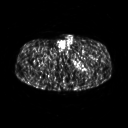
FDG PET of an extremity soft-tissue mass (from a PET/CT study), one axial slice. Position 263 of 267 along the scan axis. 3.27 mm slice thickness. 128 × 128 image matrix, field of view 500 × 500 mm. Patient: male, 27 years. From the clinical record (not read from this slice): histological type: extraskeletal osteosarcoma; grade: high; site of the primary tumour: left adductur.
Annotated regions visible in this slice (expert contour drawn on MRI and transferred to this co-registered scan by the dataset authors):
- gross tumour volume (mass): bounding box (x1, y1, x2, y2) in pixels: (70, 49, 97, 75)